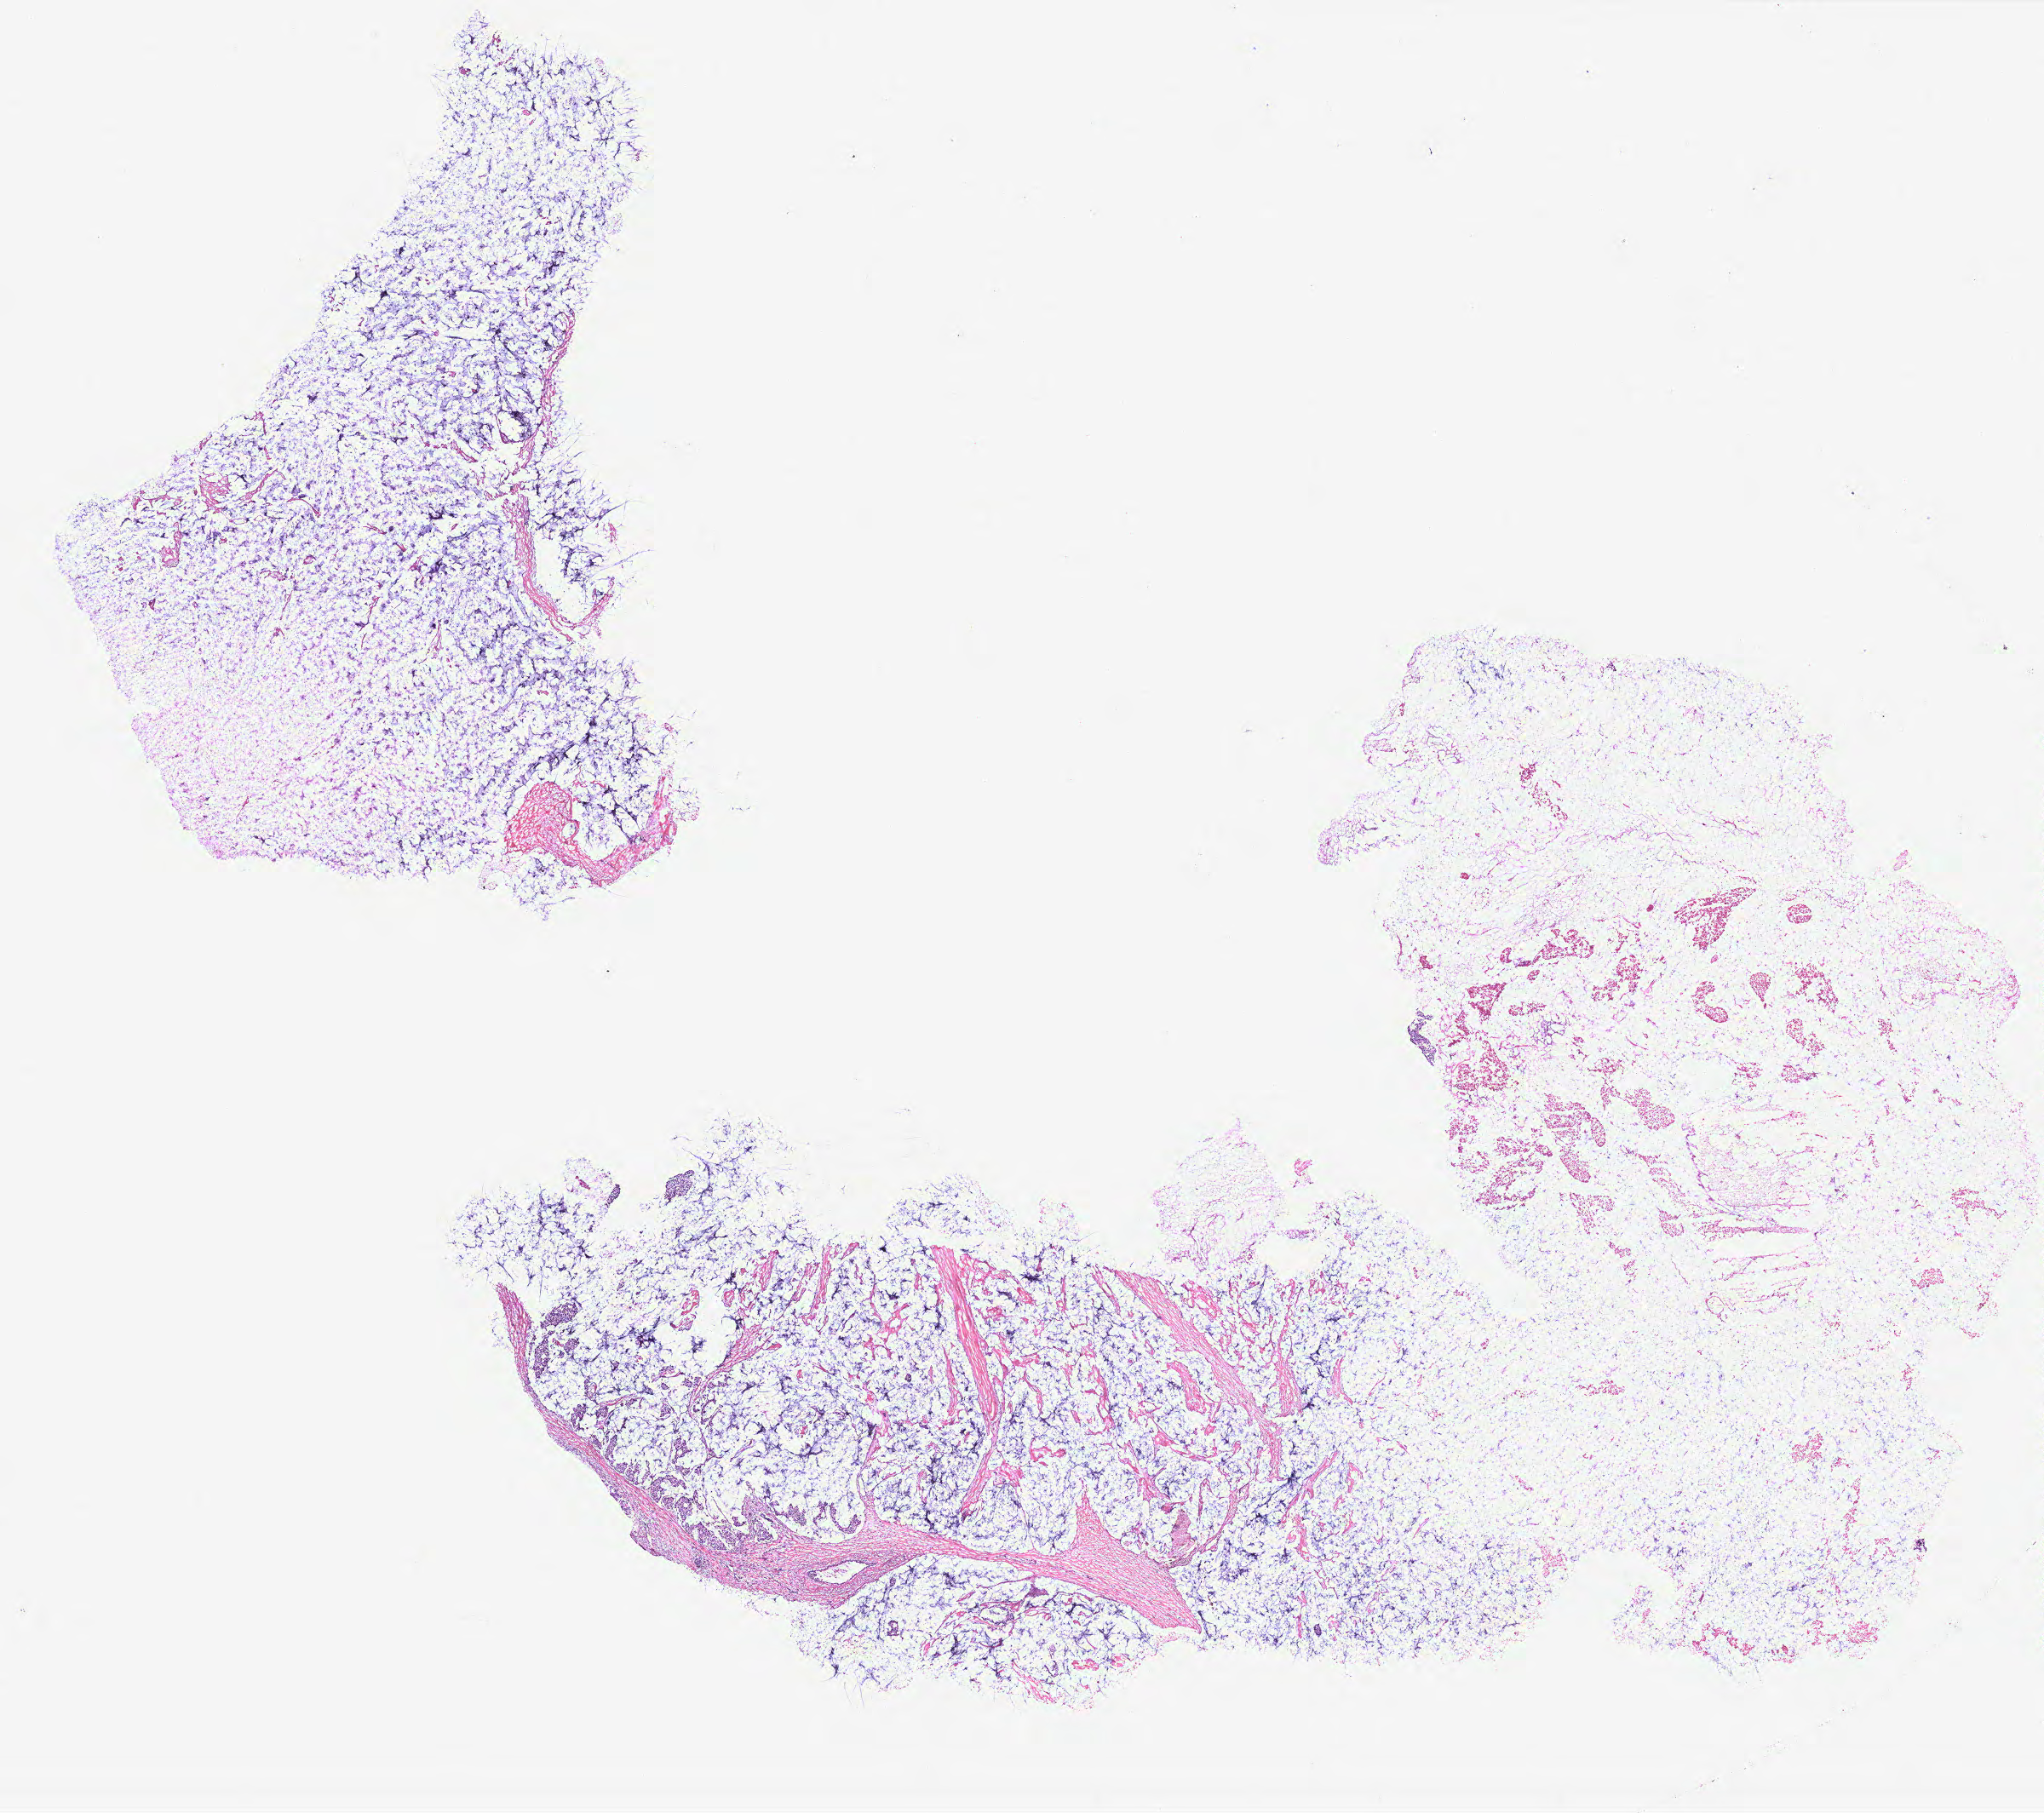
Whole-slide histology image, H&E-stained — shown as a low-resolution overview of the whole scanned area (about 19.2 x 17.0 mm); breast, tissue type not recorded.
Patient diagnosis (cohort enrolment): breast cancer (breast).